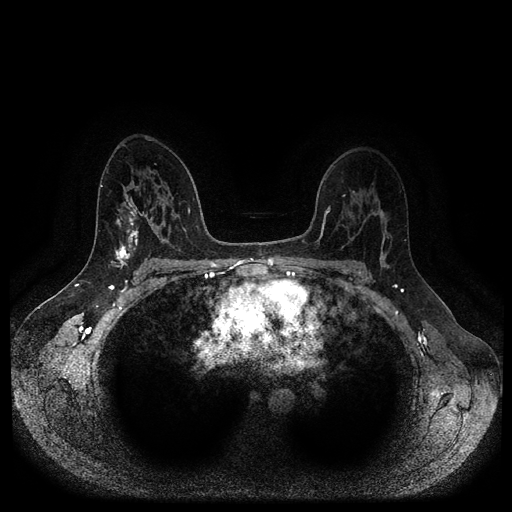
Breast MRI (dynamic contrast-enhanced, multi-phase), one axial slice. Position 64 of 116 along the scan axis. Dynamic contrast-enhanced series, time point 2 of 5 at this slice position (early post-contrast). 1.5 T. TE 2.6 ms, TR 5.3 ms. 2 mm slice thickness. 512 × 512 image matrix, field of view 360 × 360 mm. Female patient, age 45 years.
Outlined on this slice (semi-automatic segmentation, software-assisted and operator-edited):
- breast lesion (labelled benign in the annotation): bounding box [x1, y1, x2, y2] px = [116, 216, 139, 250]
- breast lesion (labelled 'tumour' in the annotation; benign lesions carry a separate 'benign' label): [114, 244, 132, 271]